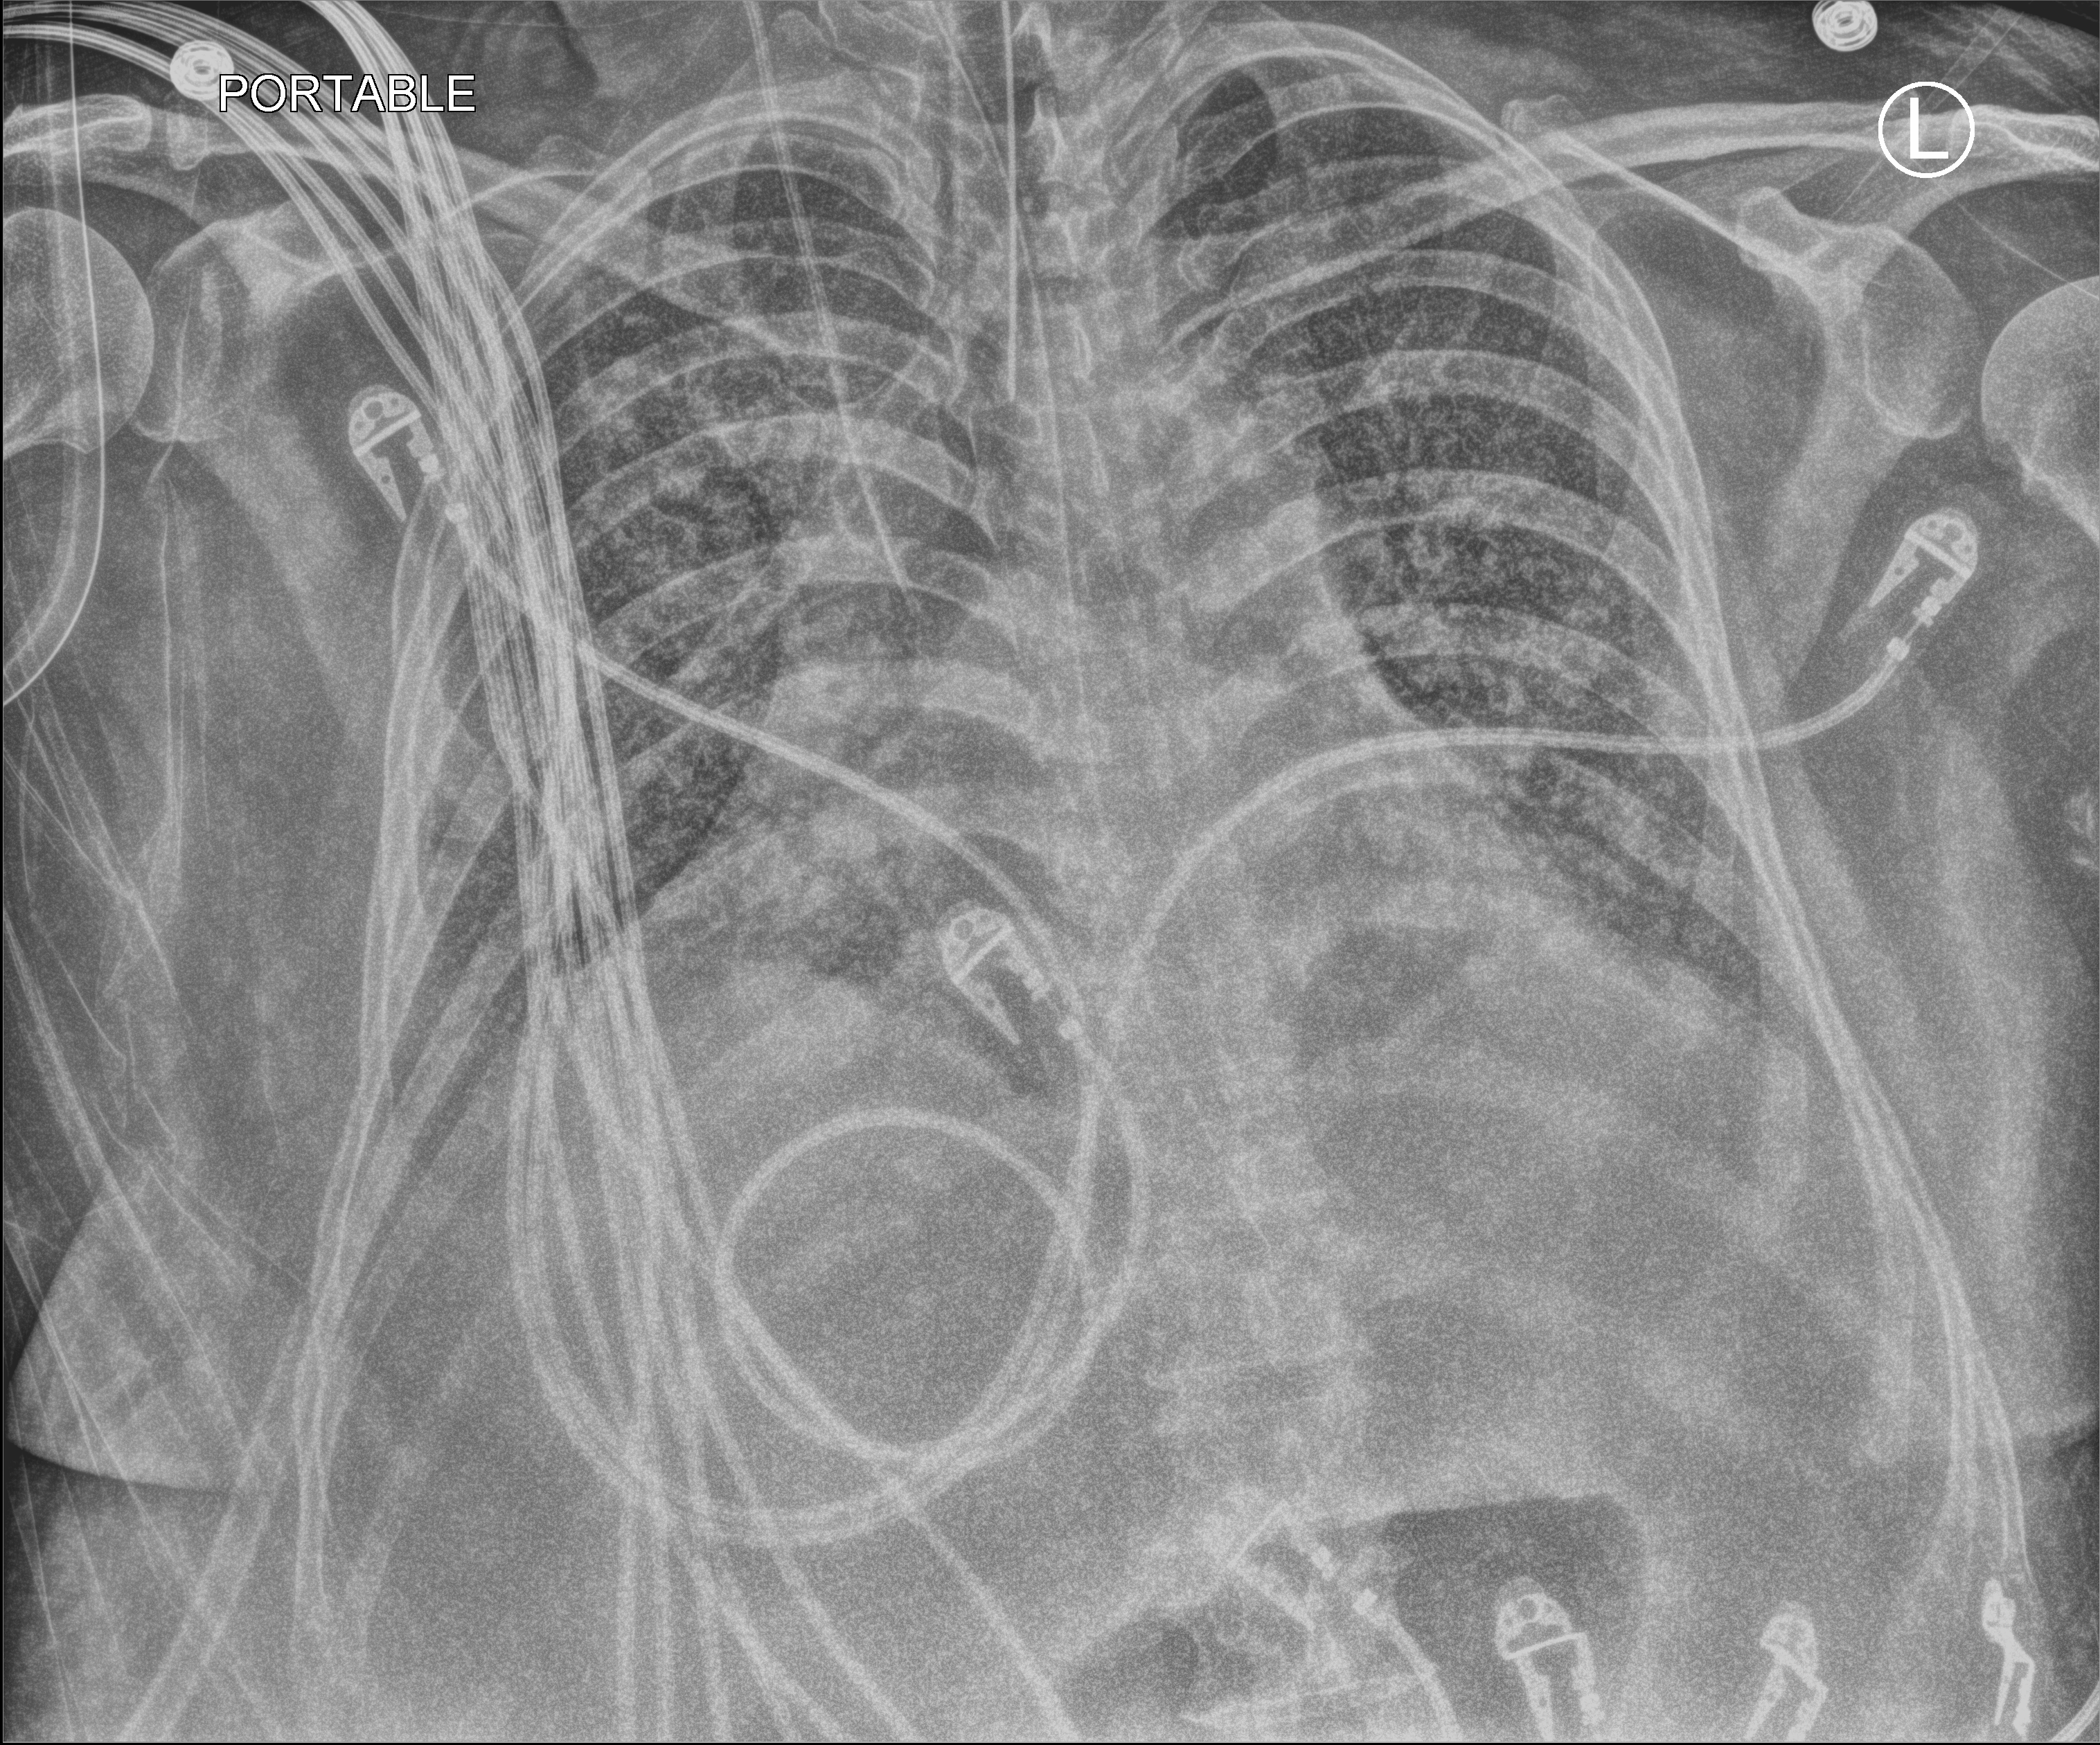
Bedside chest radiograph (computed radiography); anteroposterior (AP) projection. Patient hospitalised with COVID-19, aged 18–59 years.
Hospital-stay facts (about this admission, not read from this image; timing relative to this image not recorded): chronic kidney disease (admission record): no.